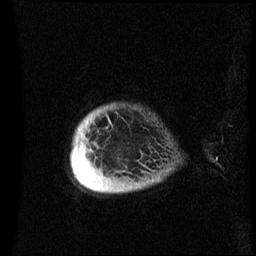
Breast MRI (dynamic contrast-enhanced), one sagittal slice; position 1 of 60 along the scan axis; dynamic contrast-enhanced series, image 2 of 3 at this slice position (ordered by acquisition); 1.5 T; TE 4.2 ms, TR 8.4 ms; 2.4 mm slice thickness; 256 × 256 image matrix, field of view 230 × 230 mm. Female patient, age 49 years.
Structures marked on this image (semi-automatic segmentation, software-assisted and operator-edited):
- analysis volume of interest (the breast-tissue region the enhancement analysis was run in; not a lesion): bounding box <71,106,170,192> (left, top, right, bottom; pixels)
- tumour enhancement mask (voxels above the 70 % enhancement threshold inside the analysis volume of interest): <71,158,78,176>